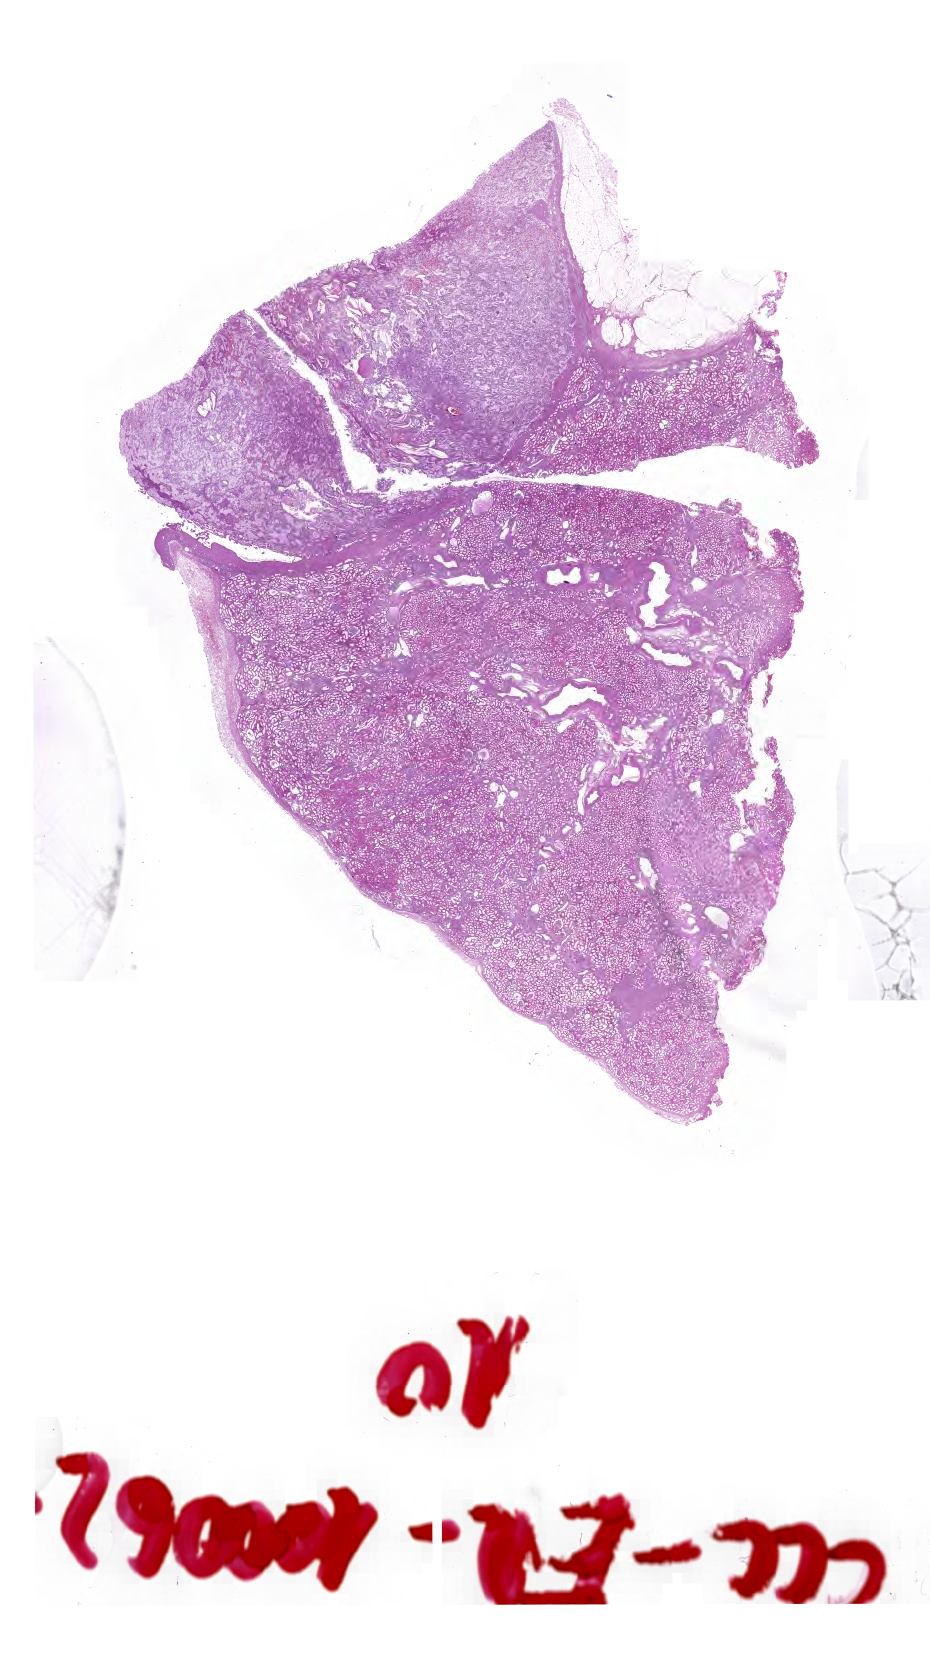
Whole-slide histology image, H&E-stained — a low-resolution overview of the entire scanned area, about 23.2 x 41.4 mm (acquisition: 40x scan). Formalin-fixed paraffin-embedded (FFPE) diagnostic section. Sample: primary tumour, kidney. Male patient; age at initial diagnosis 53 years.
* diagnosis: Papillary adenocarcinoma, NOS